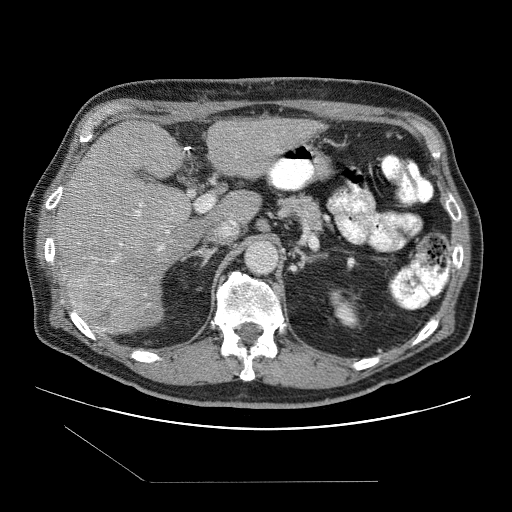
Contrast-enhanced abdominal CT (liver protocol), one axial slice; one of 2 acquisitions stored at this slice position; soft-tissue window (W 400 / L 40 HU); 2.5 mm slice thickness; 512 × 512 image matrix, field of view 400 × 400 mm. From the clinical record (not read from this slice): diagnosis: hepatocellular carcinoma (patient treated with transarterial chemoembolisation; whether this scan precedes or follows treatment is not stated here); TNM stage (as recorded): Stage-IIIB; Child-Pugh class: A; tumour differentiation: well differentiated.
Structures marked on this image (semi-automatic segmentation, software-assisted and operator-edited):
- liver parenchyma outside the tumour (the mass and vessels are separate outlines, so this box may not span the whole liver): bounding box (x1, y1, x2, y2) in pixels: (54, 118, 318, 332)
- mass: (68, 262, 144, 332)
- liver vessels: (79, 203, 169, 295)